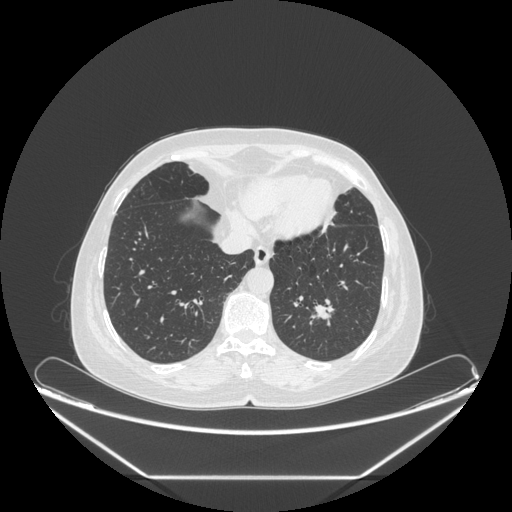
Chest CT, one axial slice; slice 70 of 241 in the series (ordered by position); 120 kVp; lung window (W 1500 / L -600 HU); 512 × 512 image matrix, field of view 451 × 451 mm. Female patient, age 63 years. From the clinical record (not read from this slice): clinical TNM (as recorded): T1c N0 M0; histopathological grade: G2-3.
Outlined on this slice (bounding box drawn by a radiologist):
- lung tumour (recorded histology: adenocarcinoma): bounding box (x1, y1, x2, y2) in pixels: (307, 298, 342, 341)